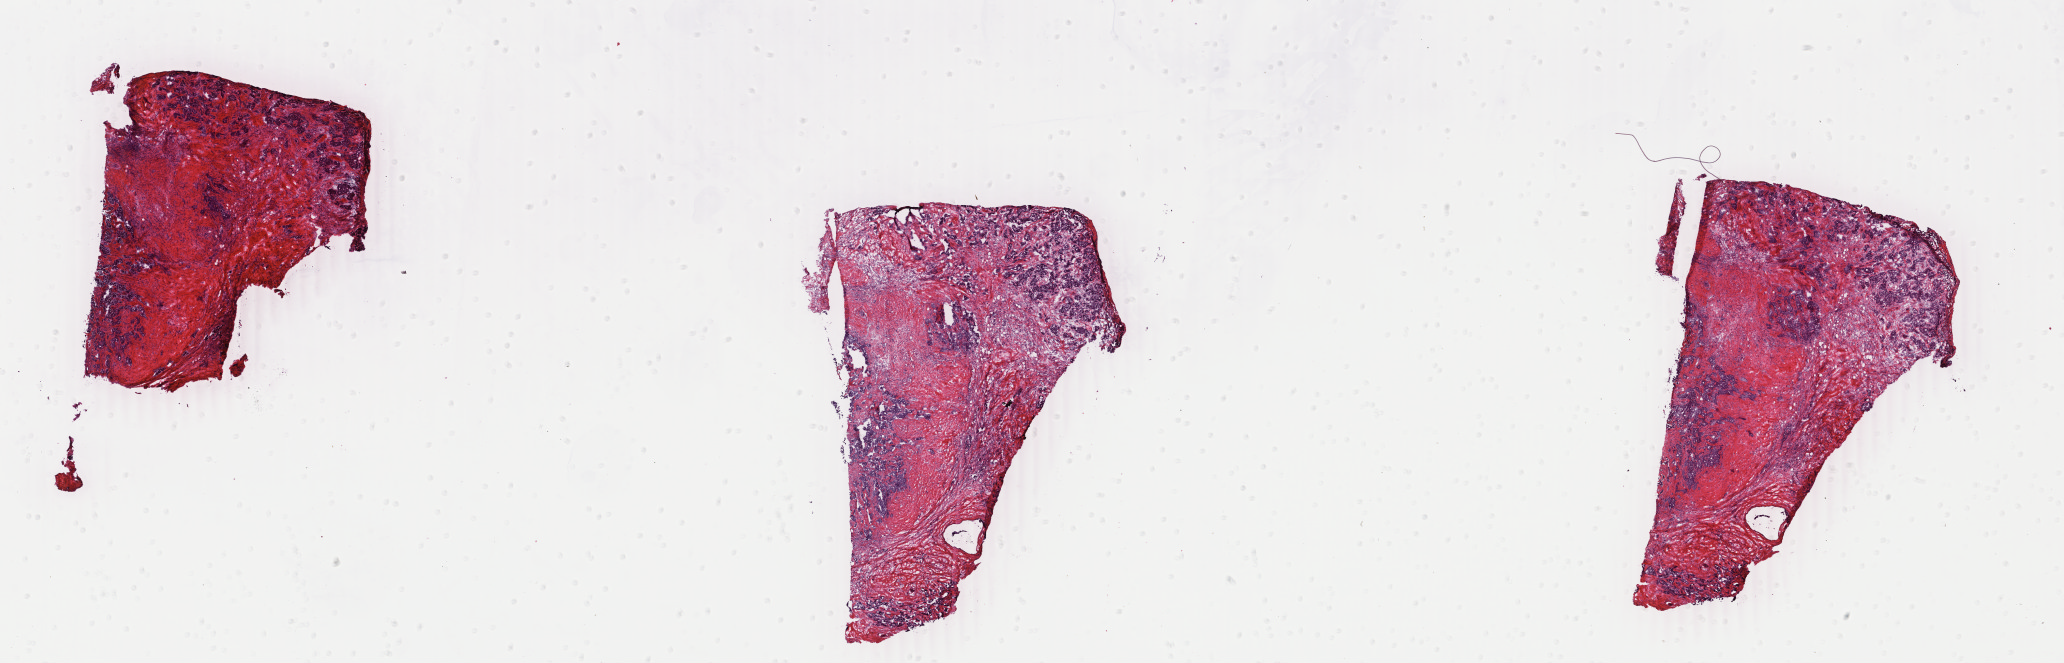
Whole-slide histology image, H&E-stained — whole scanned area (about 32.8 x 10.5 mm) shown as a low-resolution overview. Frozen section. Sample: primary tumour, breast. Patient: female, age at initial diagnosis 42 years. Pathologist review of this section (percent, as recorded): tumour cells 45%, tumour nuclei 45%, normal cells 0%, stromal cells 54%, necrosis 1%. Inflammatory infiltration, as recorded: lymphocyte infiltration 4%, monocyte infiltration 0%, neutrophil infiltration 0%.
• lymph nodes positive (case pathology): 0 of 1 examined
• AJCC pathologic stage: IA (6th edition)
• histologic diagnosis: Infiltrating duct carcinoma, NOS